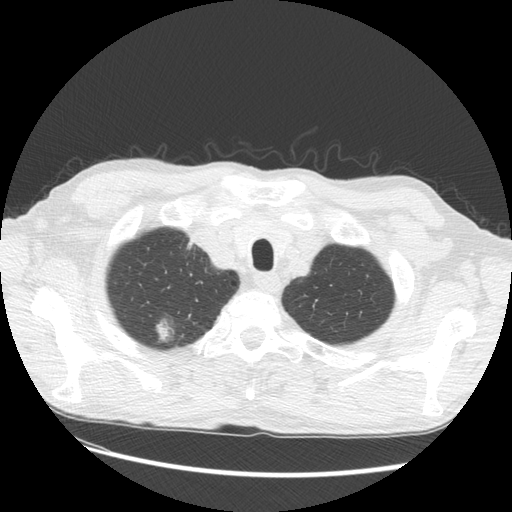
Low-dose screening chest CT, one axial slice; slice 120 of 133 in the series (ordered by position); reconstruction kernel STANDARD; 120 kVp; lung window (W 1500 / L -600 HU); 2.5 mm slice thickness; 512 × 512 image matrix, field of view 360 × 360 mm.
Annotated regions visible in this slice (outlined manually by an expert reader):
- lesion 2 (tumor, upper lobe of right lung): box from (x=156, y=319) to (x=174, y=342) px